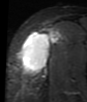
MRI of an extremity soft-tissue mass, one axial slice. Slice 31 of 48 in the series (ordered by position). STIR. MR volume resampled by the dataset authors to the PET/CT grid (not the native acquisition matrix). 3.27 mm slice thickness. 87 × 102 image matrix, field of view 85 × 100 mm. Female patient. From the clinical record (not read from this slice): histological type: synovial sarcoma; grade: intermediate; site of the primary tumour: right thigh.
Outlined on this slice (expert contour drawn on MRI and transferred to this co-registered scan by the dataset authors):
- gross tumour volume including surrounding oedema: bounding box [x1, y1, x2, y2] px = [21, 29, 57, 73]
- gross tumour volume (mass): [21, 31, 55, 73]